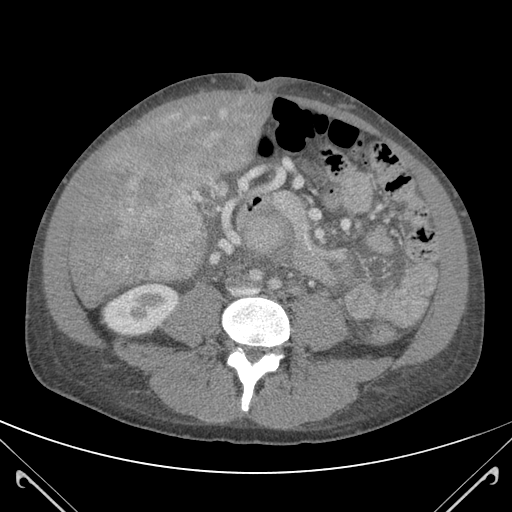
Contrast-enhanced abdominal CT (liver protocol), one axial slice. Slice 35 of 118 in the series (ordered by position). 120 kVp. Soft-tissue window (W 400 / L 40 HU). 3 mm slice thickness. 512 × 512 image matrix. From the clinical record (not read from this slice): diagnosis: hepatocellular carcinoma (patient treated with transarterial chemoembolisation; whether this scan precedes or follows treatment is not stated here); TNM stage (as recorded): Stage-IIIB; Child-Pugh class: A.
Outlined on this slice (semi-automatically segmented with operator editing):
- mass: bounding box <87,93,257,280> (left, top, right, bottom; pixels)